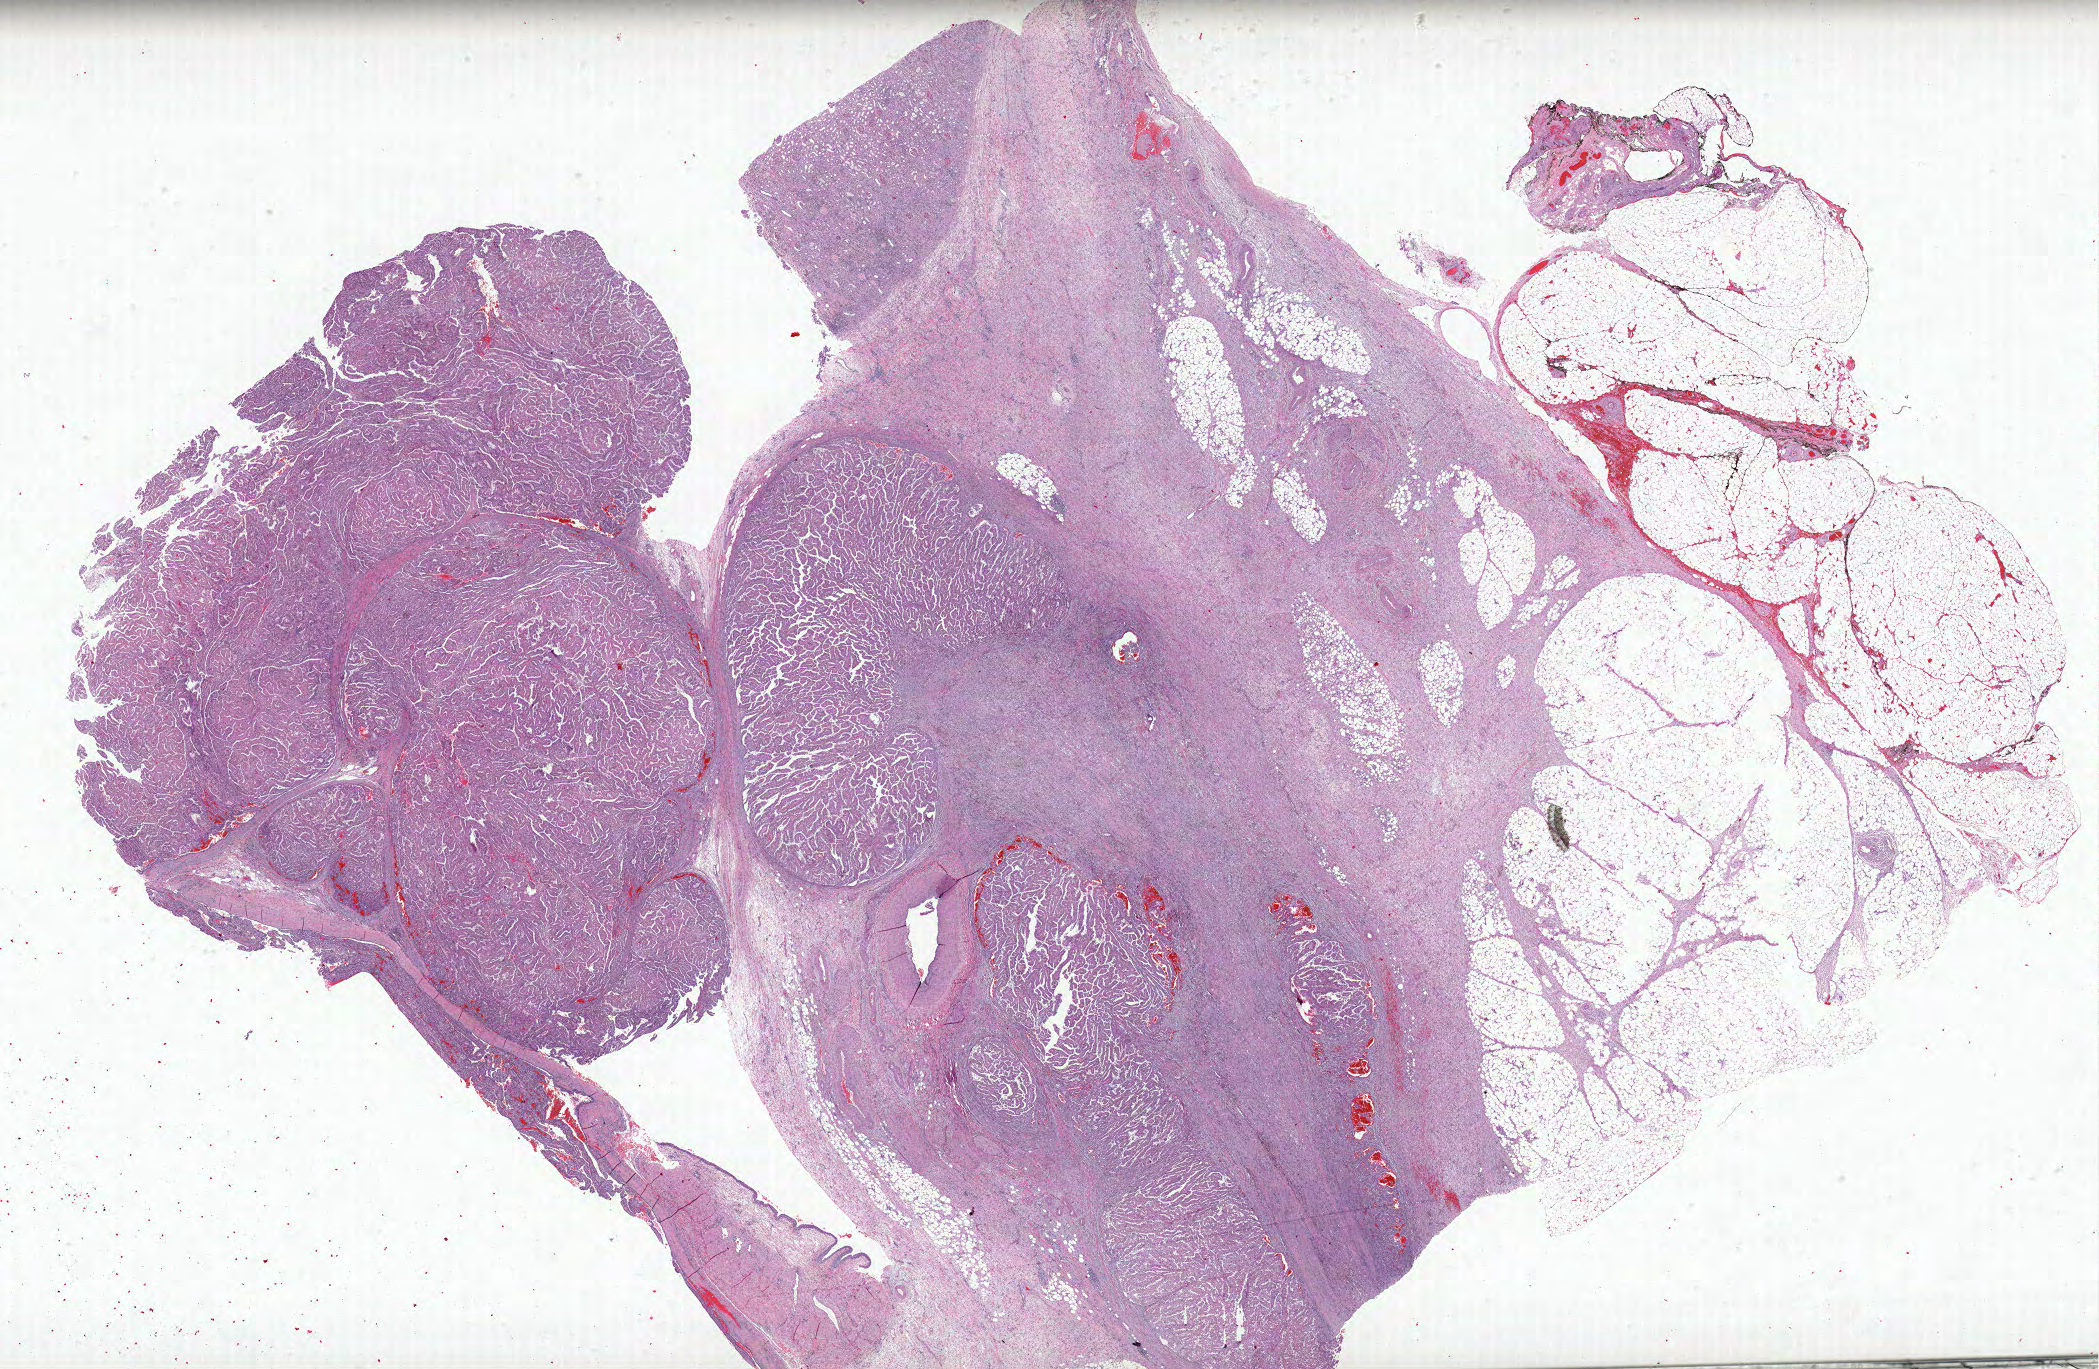
H&E whole-slide image, shown as a low-resolution overview of the whole scanned area (about 33.6 x 21.9 mm). FFPE section. Primary tumour sample from the kidney. Female, age 57 years at initial diagnosis.
Pathologic diagnosis: Papillary adenocarcinoma, NOS. TNM: T3b N0 M0. AJCC pathologic stage: III. Laterality: right. Lymph nodes positive (case pathology): 0 of 11 examined.